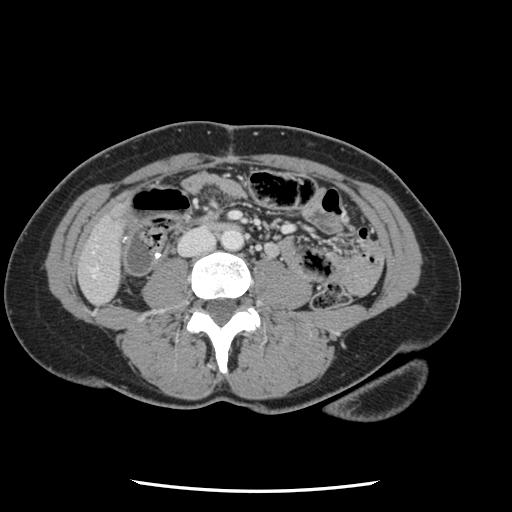
Contrast-enhanced abdominal CT, one axial slice. Slice 9 of 134 in the series (ordered by position). Intravenous contrast given. Soft-tissue window (W 400 / L 40 HU). 512 × 512 image matrix, field of view 330 × 330 mm. Female patient, age 43 years. From the clinical record (not read from this slice): diagnosis: colorectal cancer liver metastases, imaged before liver resection; multiple liver metastases: yes; largest metastasis: 3.4 cm; disease in both lobes: yes.
Annotated regions visible in this slice (expert manual segmentation):
- liver: bounding box <80,215,123,304> (left, top, right, bottom; pixels)
- planned liver remnant (the part of the liver to remain after resection): <80,215,122,304>